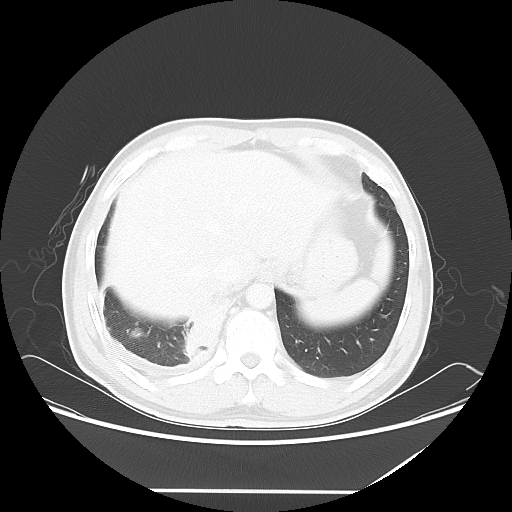
Chest CT, one axial slice; slice 13 of 60 in the series (ordered by position); reconstruction kernel LUNG; lung window (W 1500 / L -600 HU); 512 × 512 image matrix. Male patient, age 48 years. From the clinical record (not read from this slice): clinical TNM (as recorded): T3 N3 M1a.
Structures marked on this image (bounding box drawn by a radiologist):
- lung tumour (recorded histology: squamous cell carcinoma): bounding box [x1, y1, x2, y2] px = [180, 289, 231, 369]